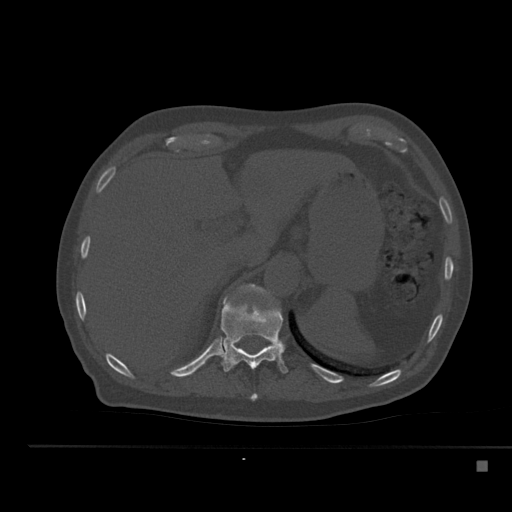
CT including the spine, one axial slice. Position 248 of 517 along the scan axis. 120 kVp. Bone window (W 1800 / L 400 HU). 512 × 512 image matrix, field of view 408 × 408 mm. Patient: male, 70 years. Case-level facts recorded for this patient, not image findings: primary cancer: renal; vertebrae with lytic lesions (as recorded): T4, T6, T10, T12, L3, L4, L5.
Structures marked on this image (semi-automatically segmented with operator editing):
- T10 vertebra: bounding box <251,393,257,401> (left, top, right, bottom; pixels)
- T11 vertebra: <220,300,288,374>
- T12 vertebra: <240,284,274,300>